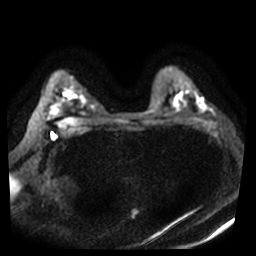
Breast MRI, one axial slice; position 30 of 40 along the scan axis; diffusion-weighted series; image 2 of 4 stored at this slice position (different b-values; order by instance number); 3 T; 5 mm slice thickness; 256 × 256 image matrix. Female patient.
Structures marked on this image (manually delineated by an expert):
- tumour on diffusion-weighted imaging: bounding box <201,105,205,109> (left, top, right, bottom; pixels)